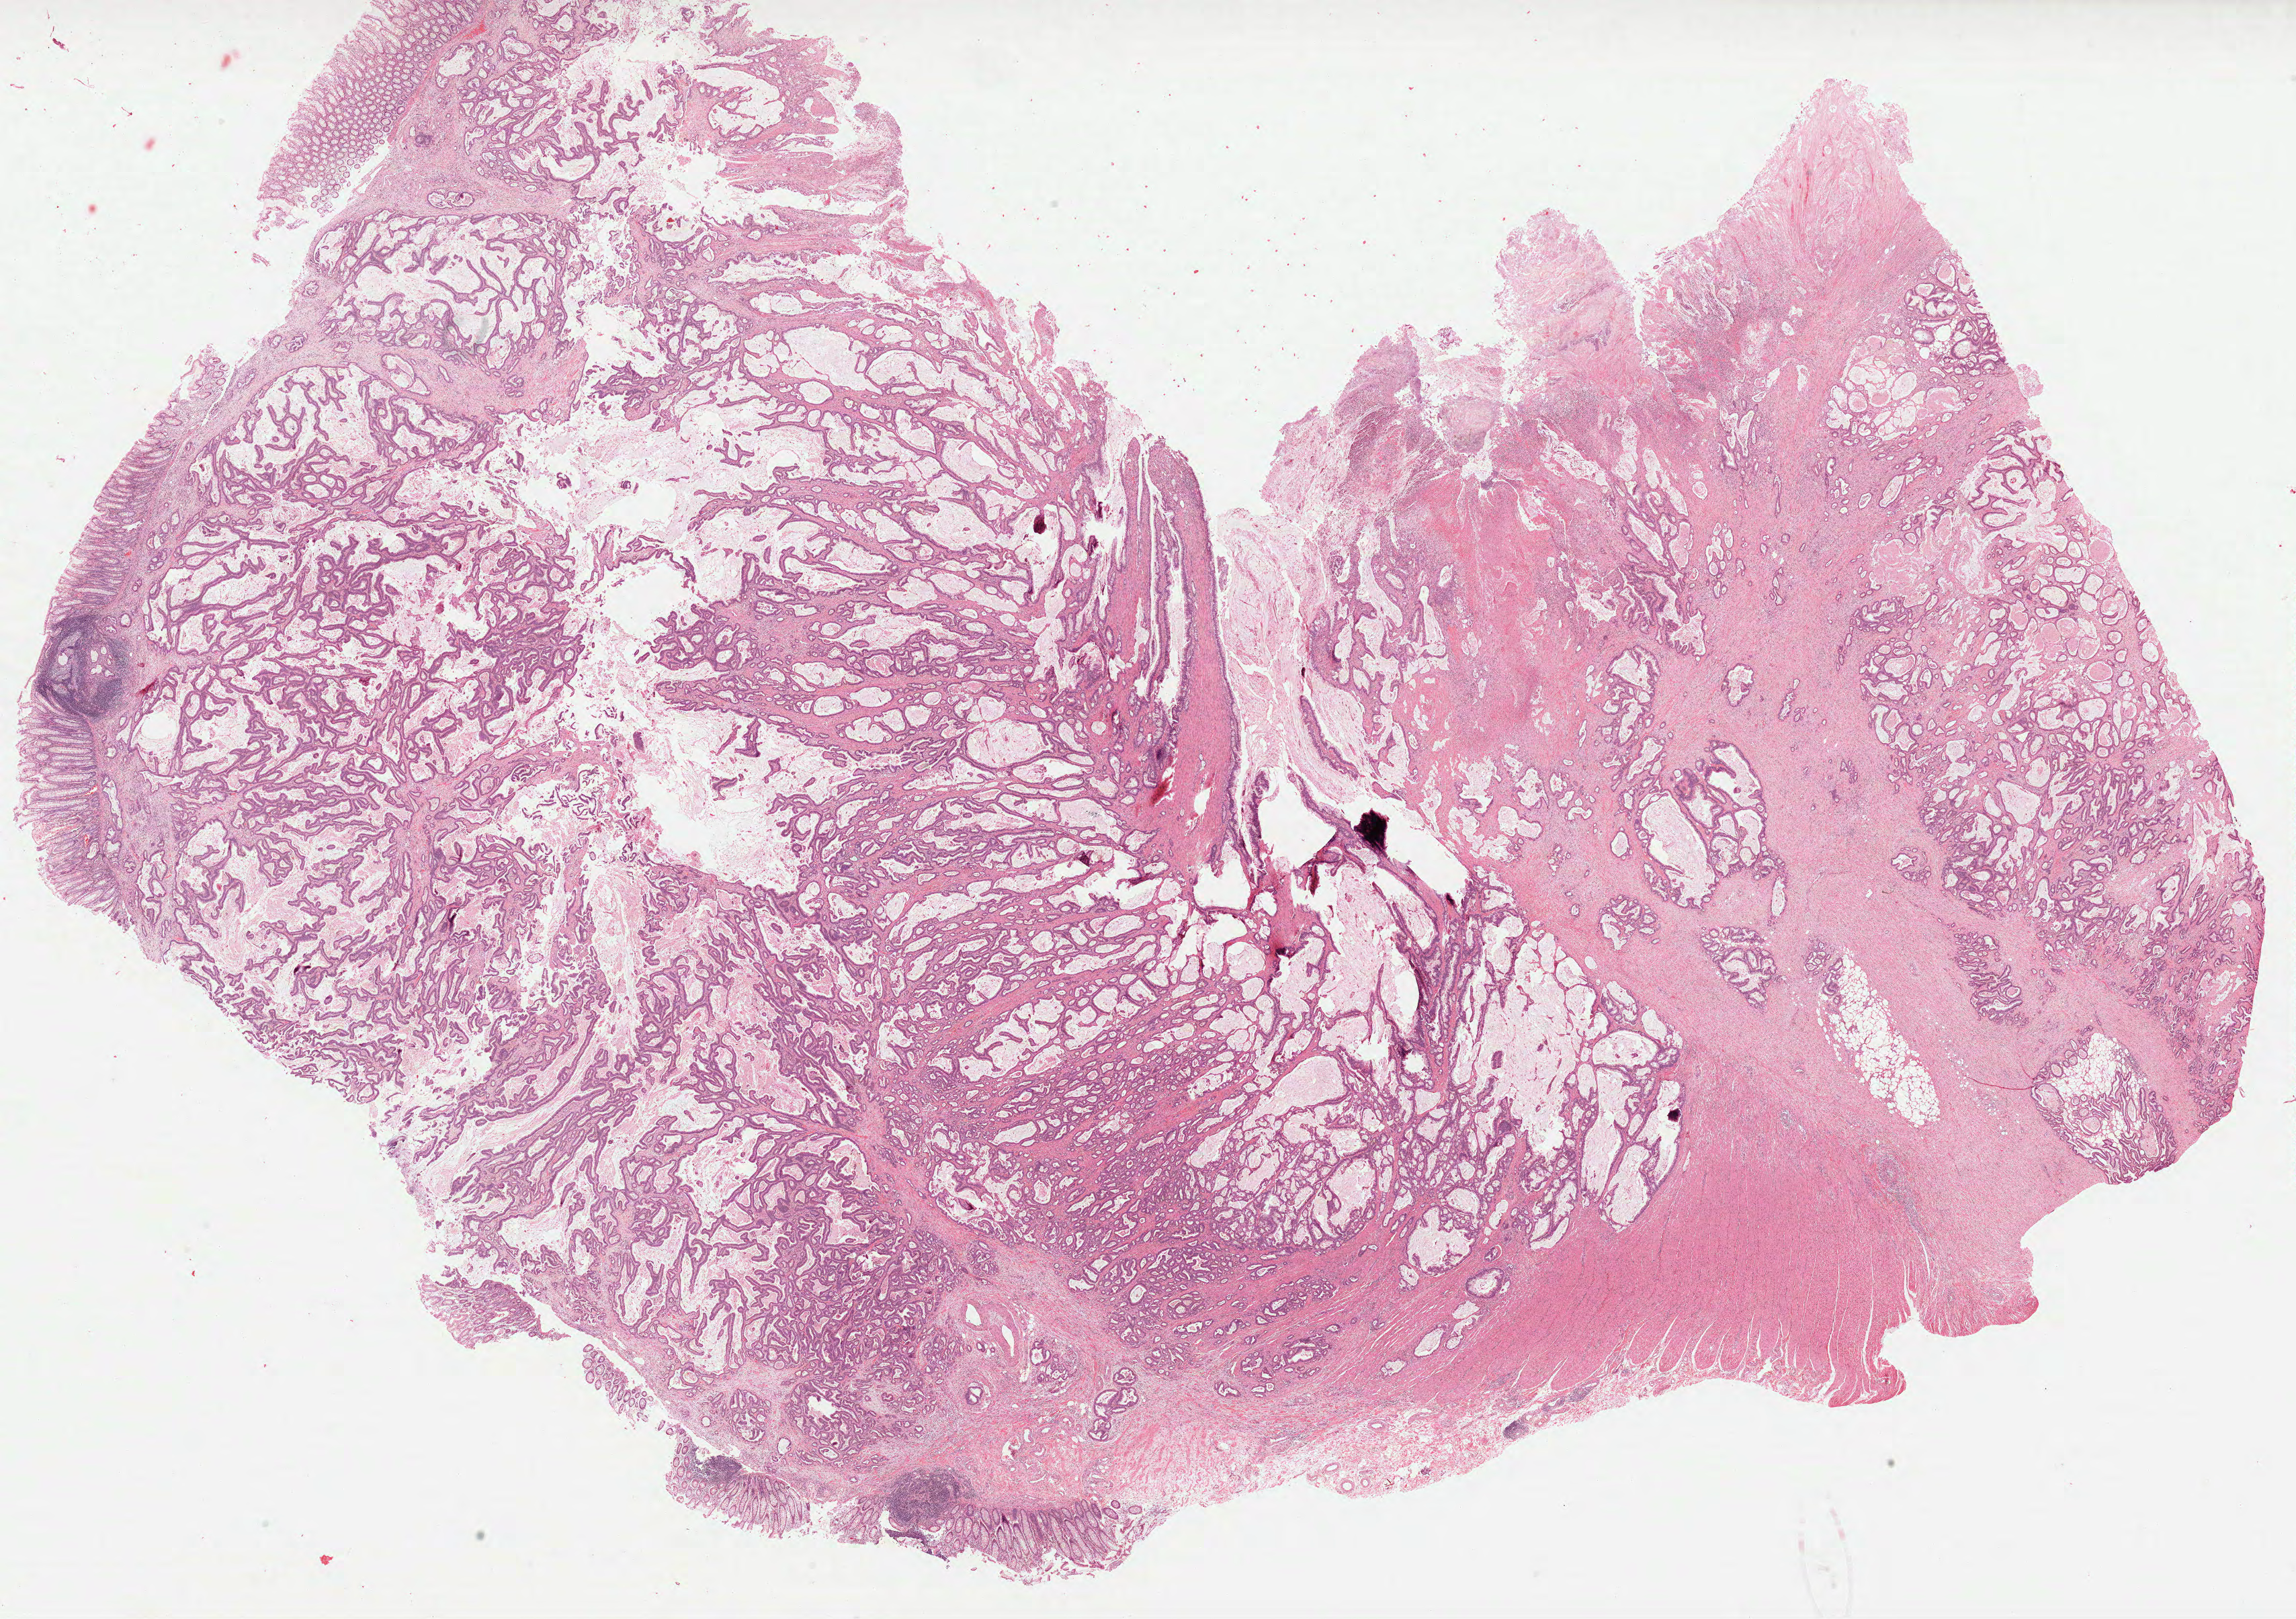
Digitized H&E-stained tissue section (whole slide), low-resolution overview of the scanned area, about 27.6 x 19.4 mm (acquisition: 40x scan). FFPE section. Sample: primary tumour, colon. Patient: female, age at initial diagnosis 41 years.
TNM: T4b N2 M0. AJCC pathologic stage: IIIC (7th edition). Pathologic diagnosis: Adenocarcinoma, NOS.